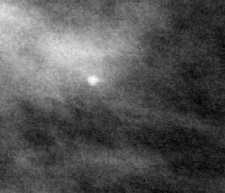
Cropped region of a digitized screen-film mammogram centred on a radiologist-marked abnormality; left breast; MLO view; BI-RADS breast density category 2 (scale 1–4).
Finding: calcifications, morphology punctate; BI-RADS assessment category 2; subtlety rating 4 on a 1 (subtle) to 5 (obvious) scale; benign; no additional work-up was recommended (benign without callback).